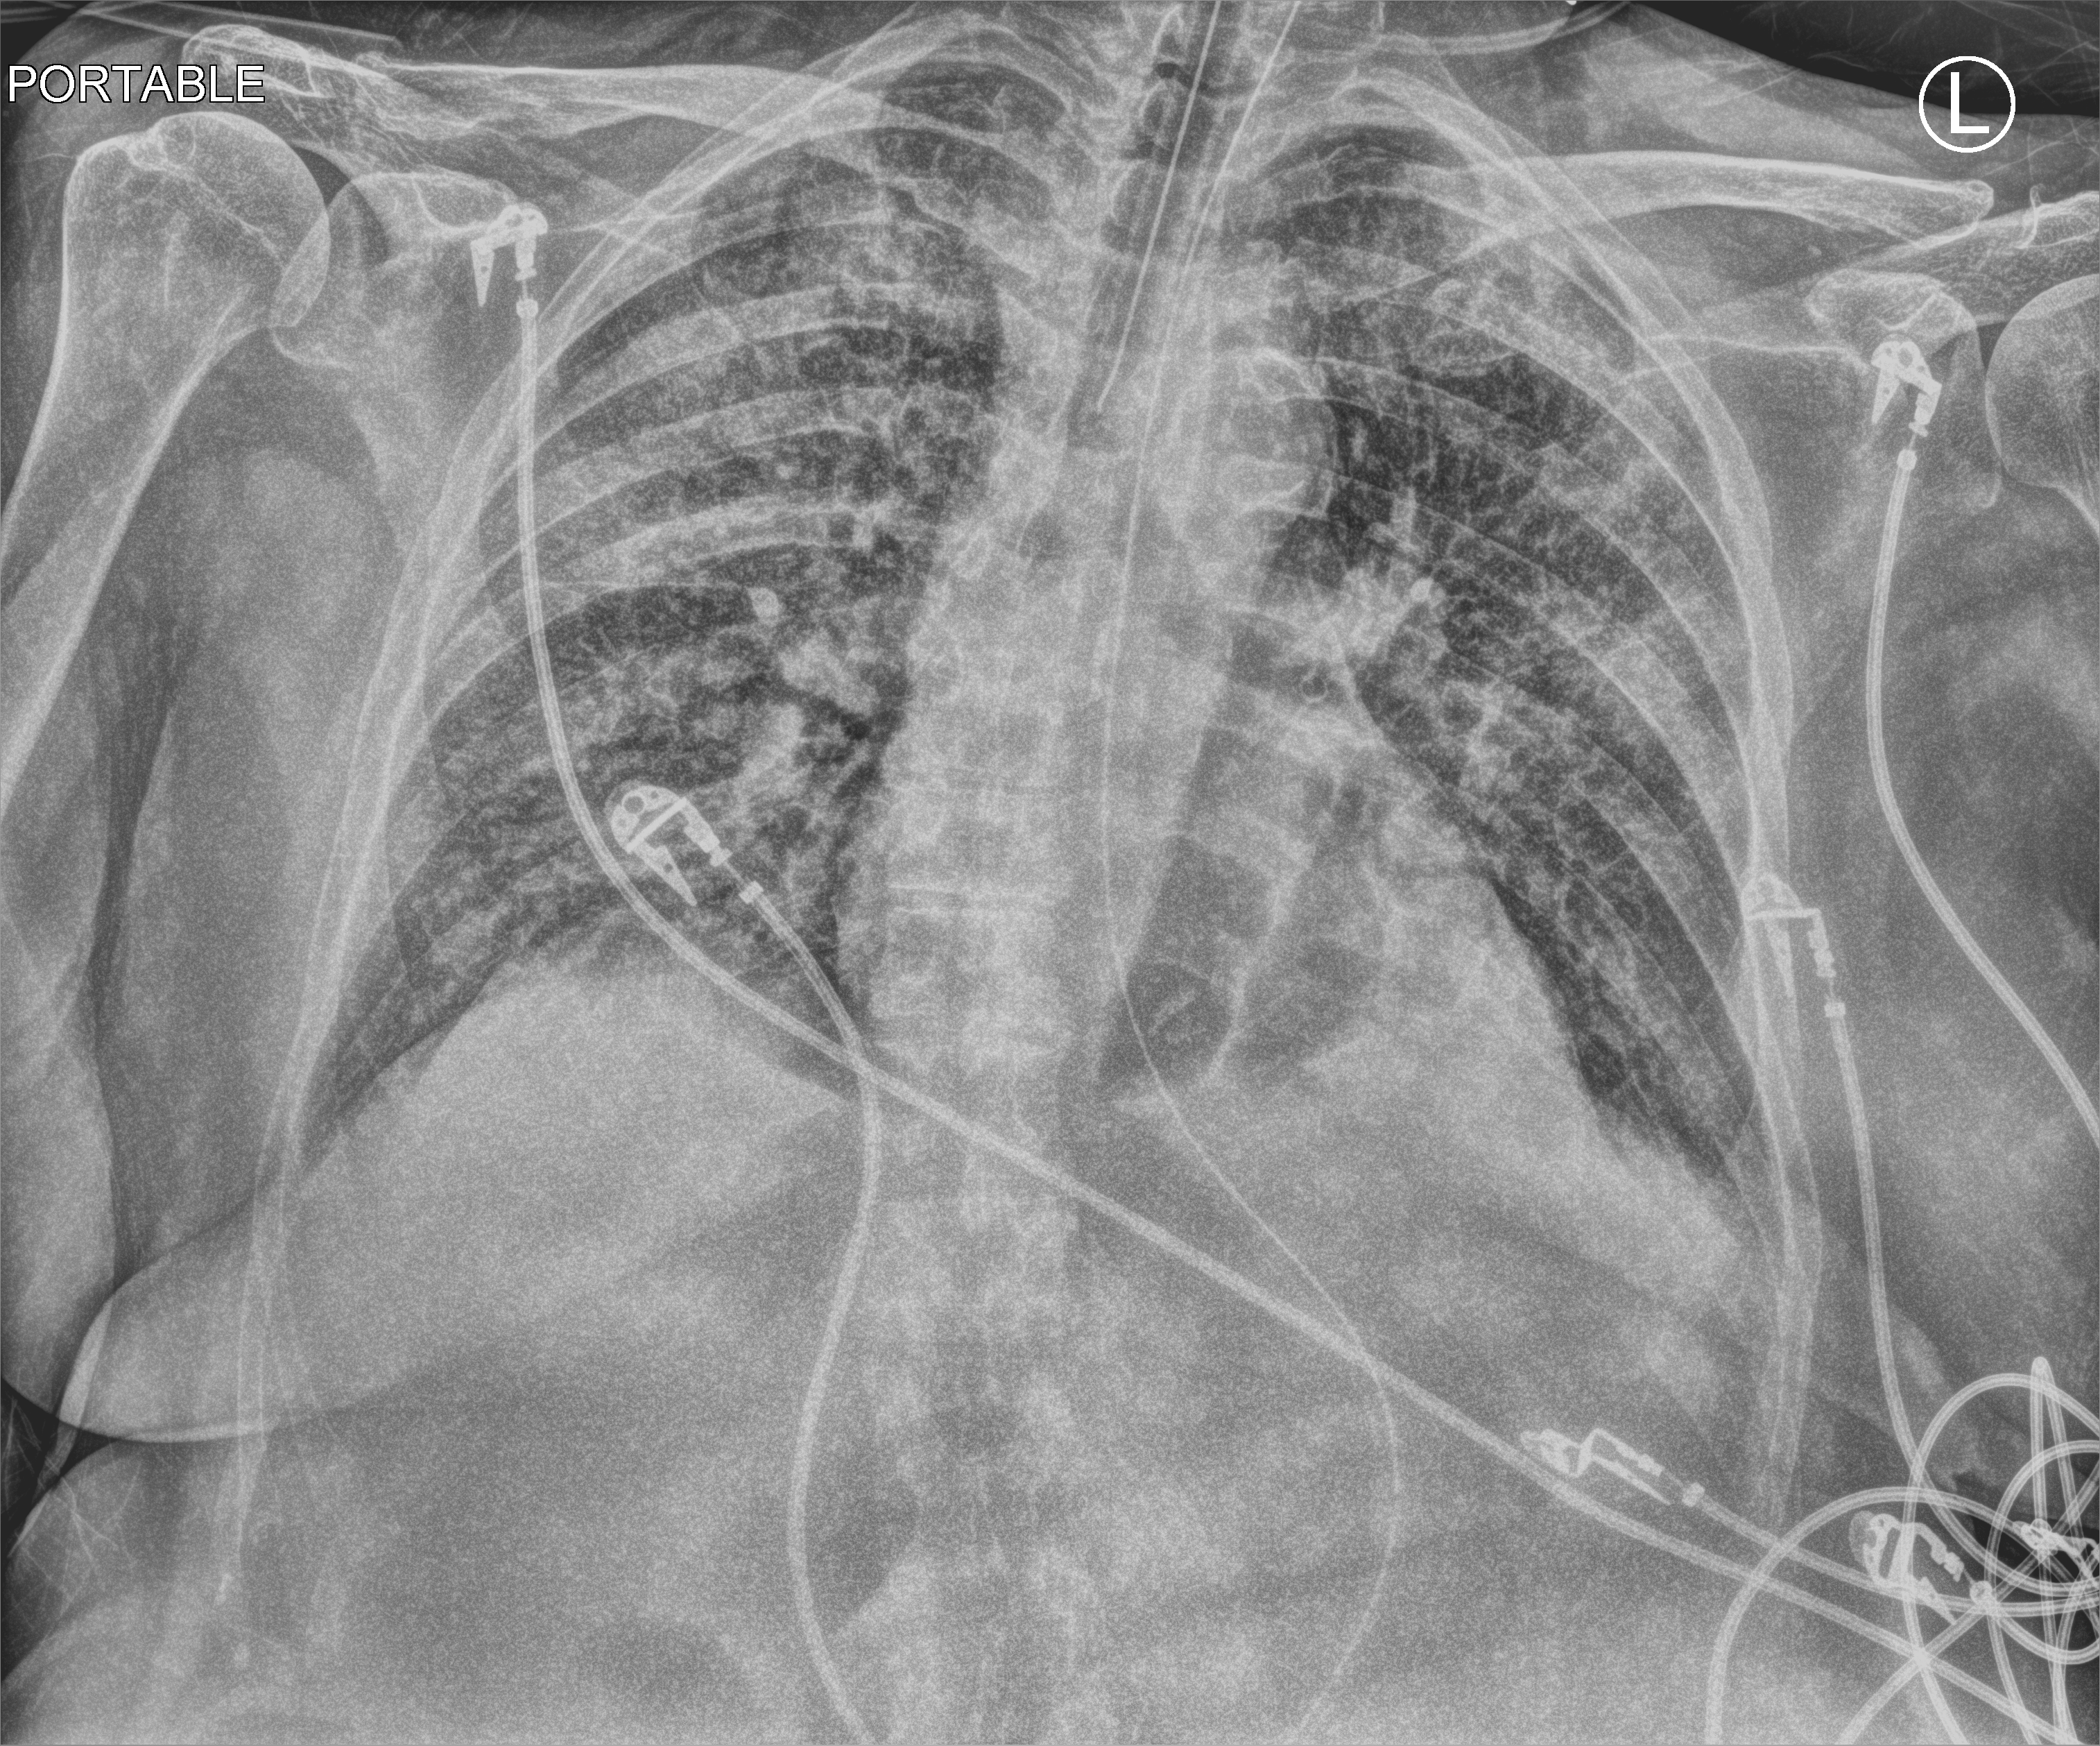
Portable chest radiograph; anteroposterior (AP) projection. Female patient hospitalised with COVID-19, age 75–90 years.
Admission-level facts for this patient (not findings on this image; timing relative to this image not recorded): smoking status (admission record): former.